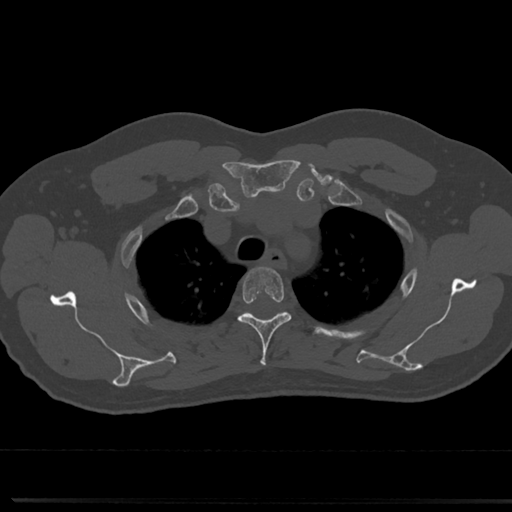
CT including the spine, one axial slice. Position 587 of 817 along the scan axis. 120 kVp. Bone window (W 1800 / L 400 HU). 0.5 mm slice thickness. 512 × 512 image matrix, field of view 355 × 355 mm. Male patient, age 61 years. Case-level facts recorded for this patient, not image findings: primary cancer: prostate.
Structures marked on this image (semi-automatic segmentation, software-assisted and operator-edited):
- T3 vertebra: bounding box [x1, y1, x2, y2] px = [239, 268, 291, 368]
- T4 vertebra: [243, 311, 286, 318]